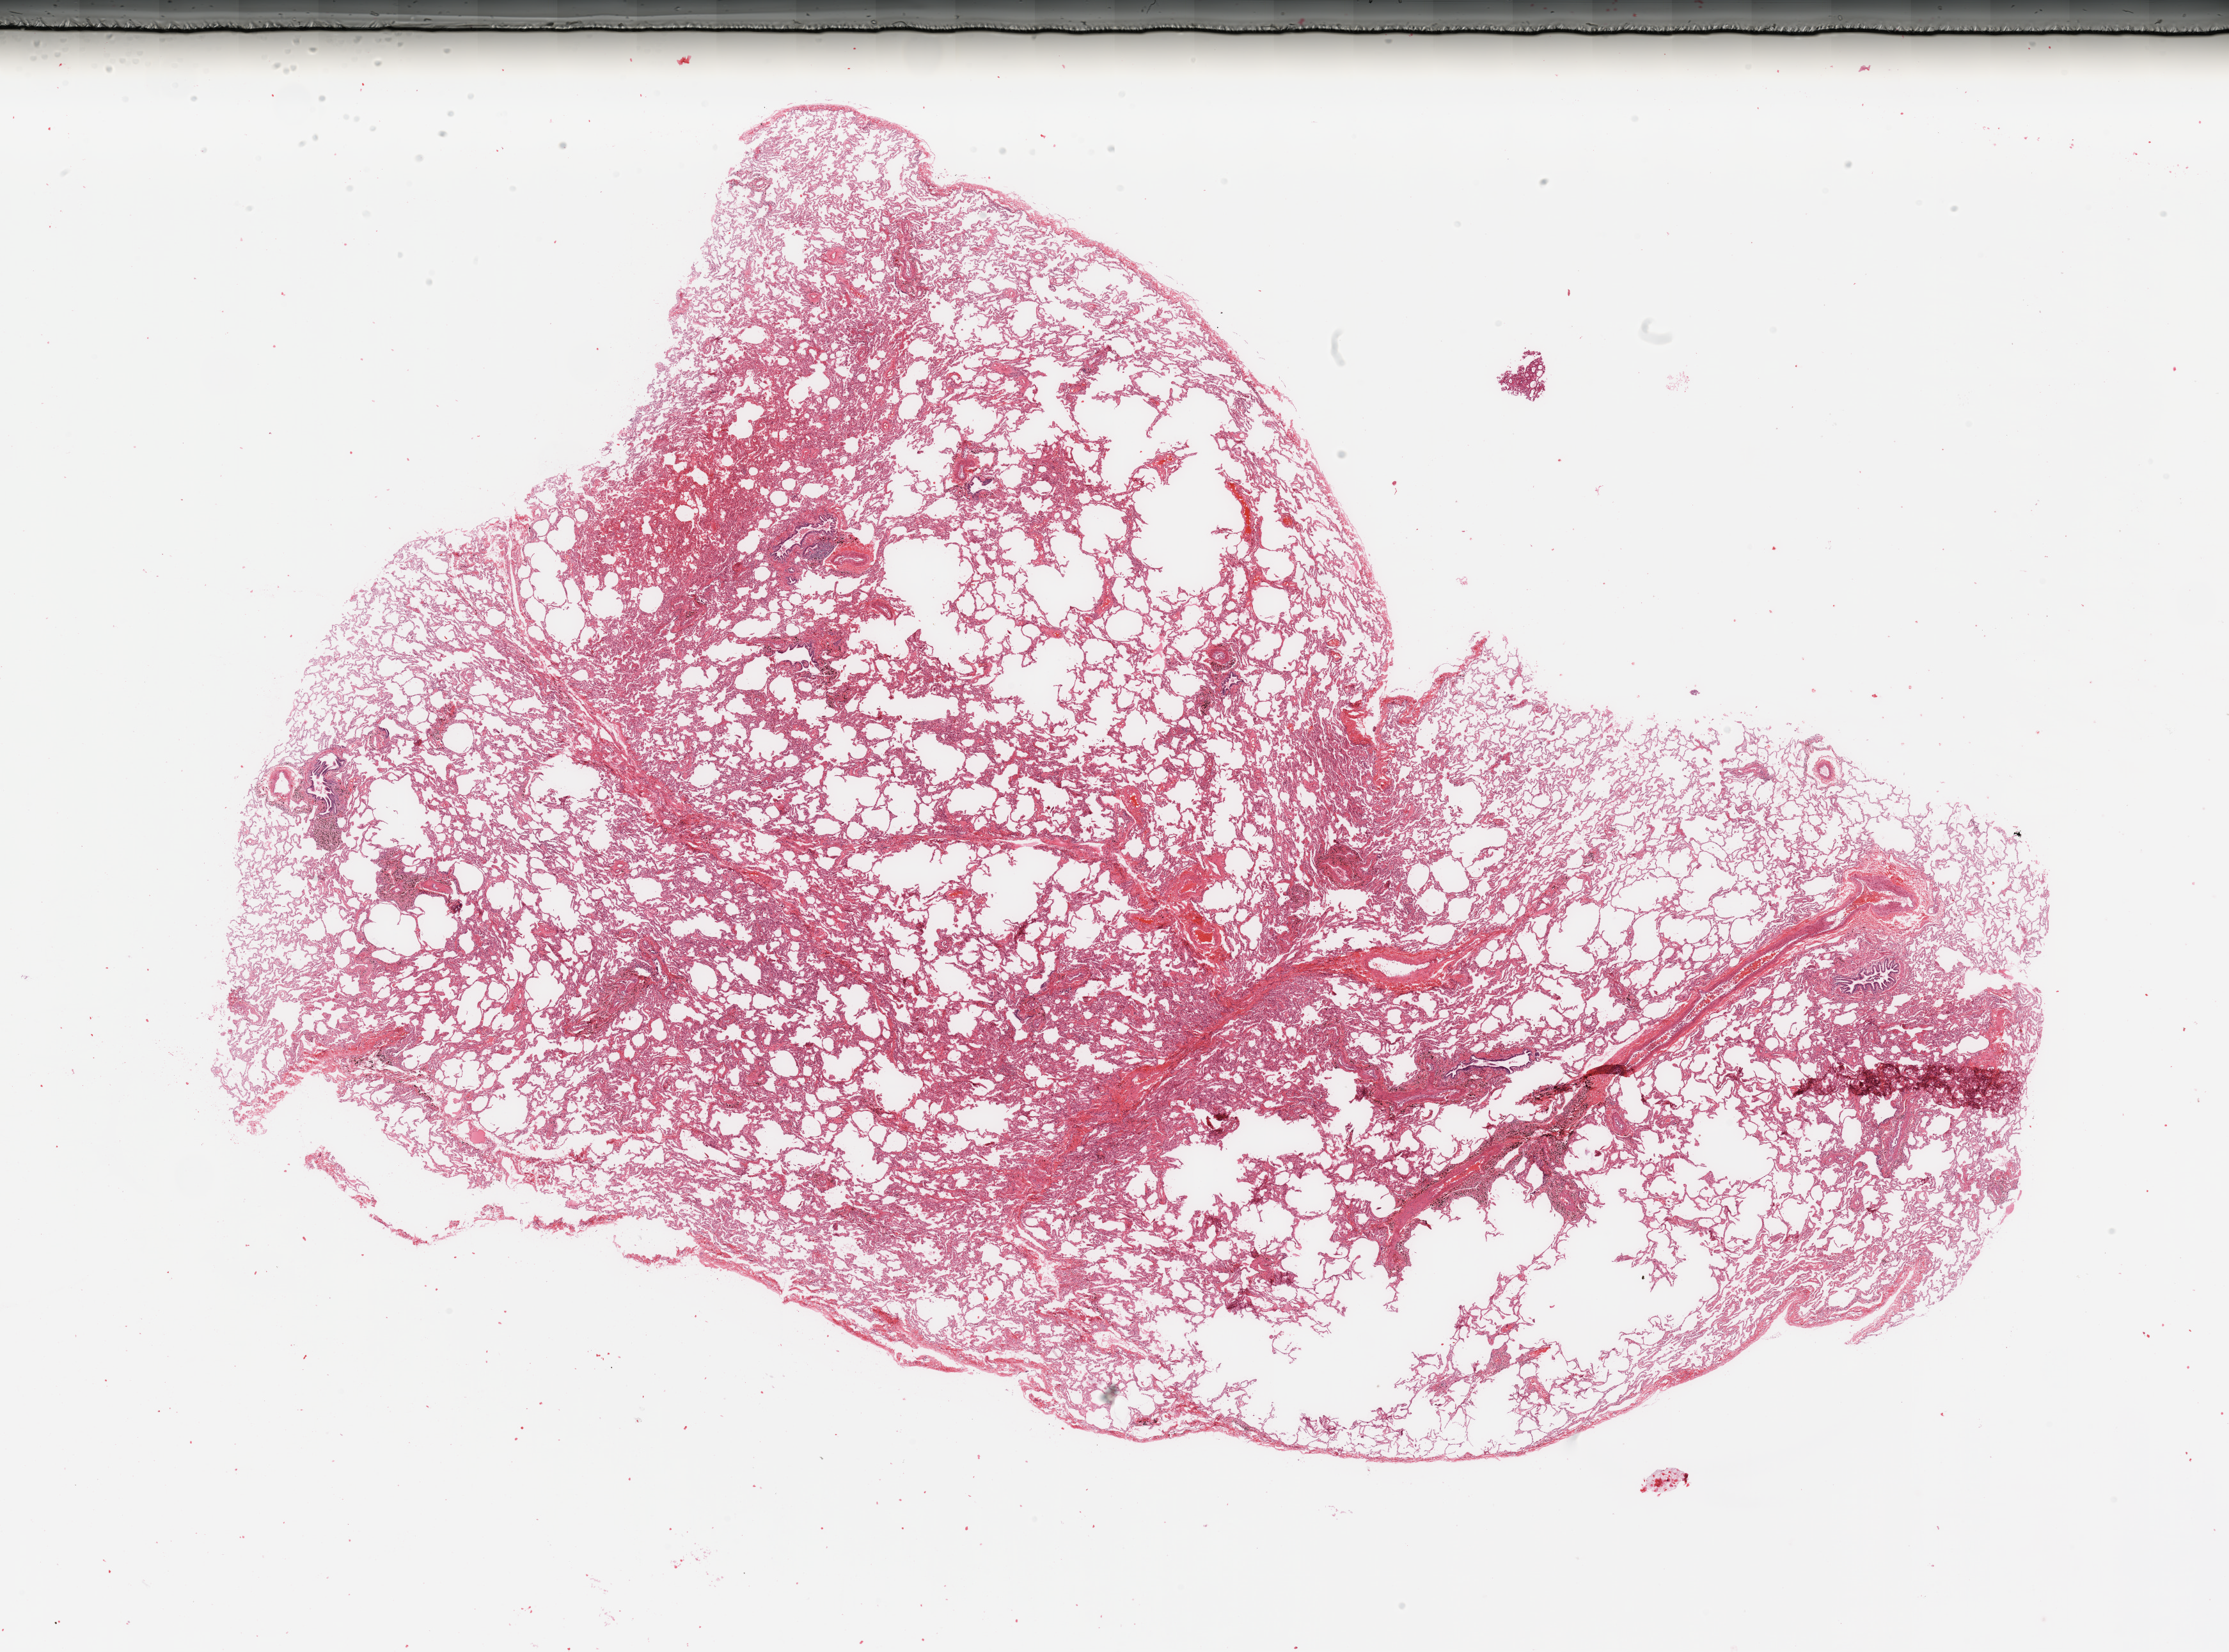
Whole-slide histology image, H&E, low-resolution overview of the scanned area, about 27.6 x 20.4 mm. Normal (non-tumour) tissue sample, sampled site: lung. Patient: female, age 61 years.
- this section: normal (non-tumour) tissue from the same patient
- patient diagnosis: Adenocarcinoma, NOS